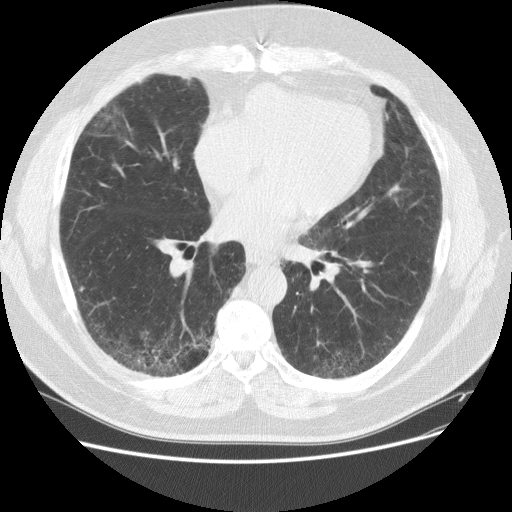
Low-dose screening chest CT, one axial slice. Position 75 of 151 along the scan axis. Reconstruction kernel STANDARD. 120 kVp. Lung window (W 1500 / L -600 HU). 2.5 mm slice thickness. 512 × 512 image matrix, field of view 378 × 378 mm.
Annotated regions visible in this slice (manually delineated by an expert):
- lesion 1 (tumor, lower lobe of right lung): bounding box (x1, y1, x2, y2) in pixels: (78, 285, 87, 294)